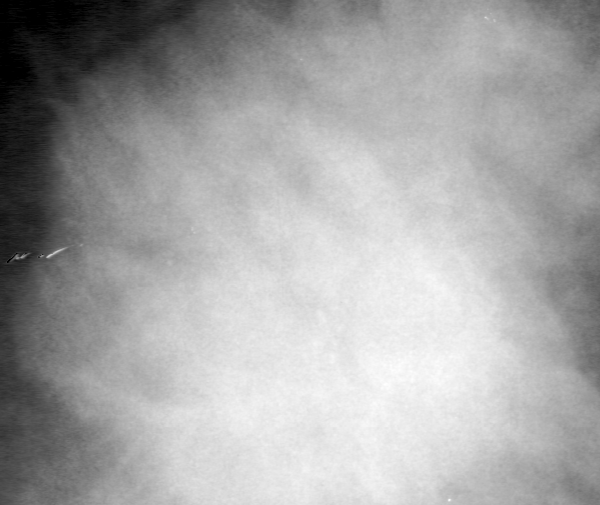
Cropped region of a digitized screen-film mammogram centred on a radiologist-marked abnormality; left breast; CC view; BI-RADS breast density category 4 (scale 1–4).
Marked abnormality: mass, shape irregular, margins spiculated; BI-RADS assessment category 5; subtlety rating 5 on a 1 (subtle) to 5 (obvious) scale; pathology (as recorded): malignant.